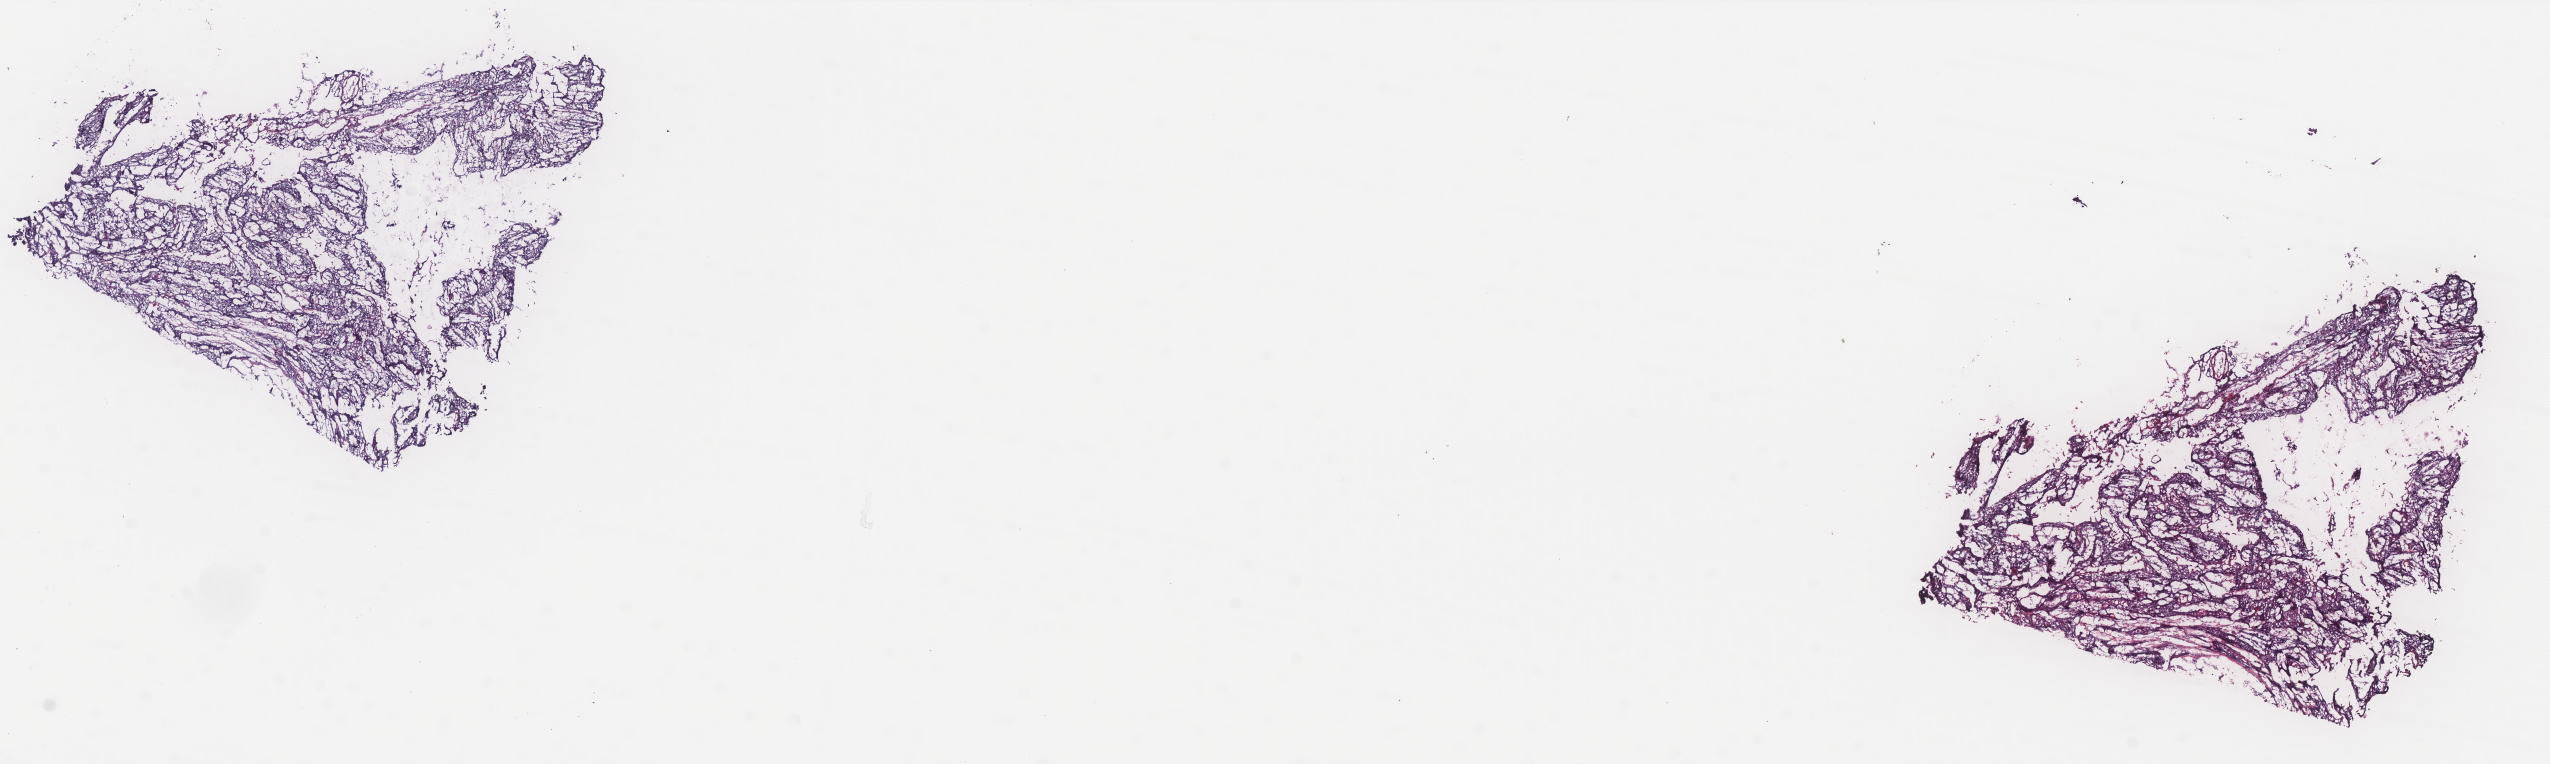
Whole-slide histology image, H&E-stained, whole scanned area (about 20.4 x 6.1 mm, slide scanned at 40x) shown as a low-resolution overview. Frozen section from the bottom of the tissue portion. Cervix, primary tumour sample. Female, age 47 years at initial diagnosis. Histologic grade: G2 (moderately differentiated). Pathologist review of this section (percent, as recorded): tumour cells 100%, tumour nuclei 65%, normal cells 0%, stromal cells 0%, necrosis 0%. Inflammatory infiltration, as recorded: lymphocyte infiltration 0%, monocyte infiltration 0%, neutrophil infiltration 0%.
Pathologic diagnosis: Squamous cell carcinoma, NOS (cervix uteri). Lymph nodes positive (case pathology): 0 of 19 examined.